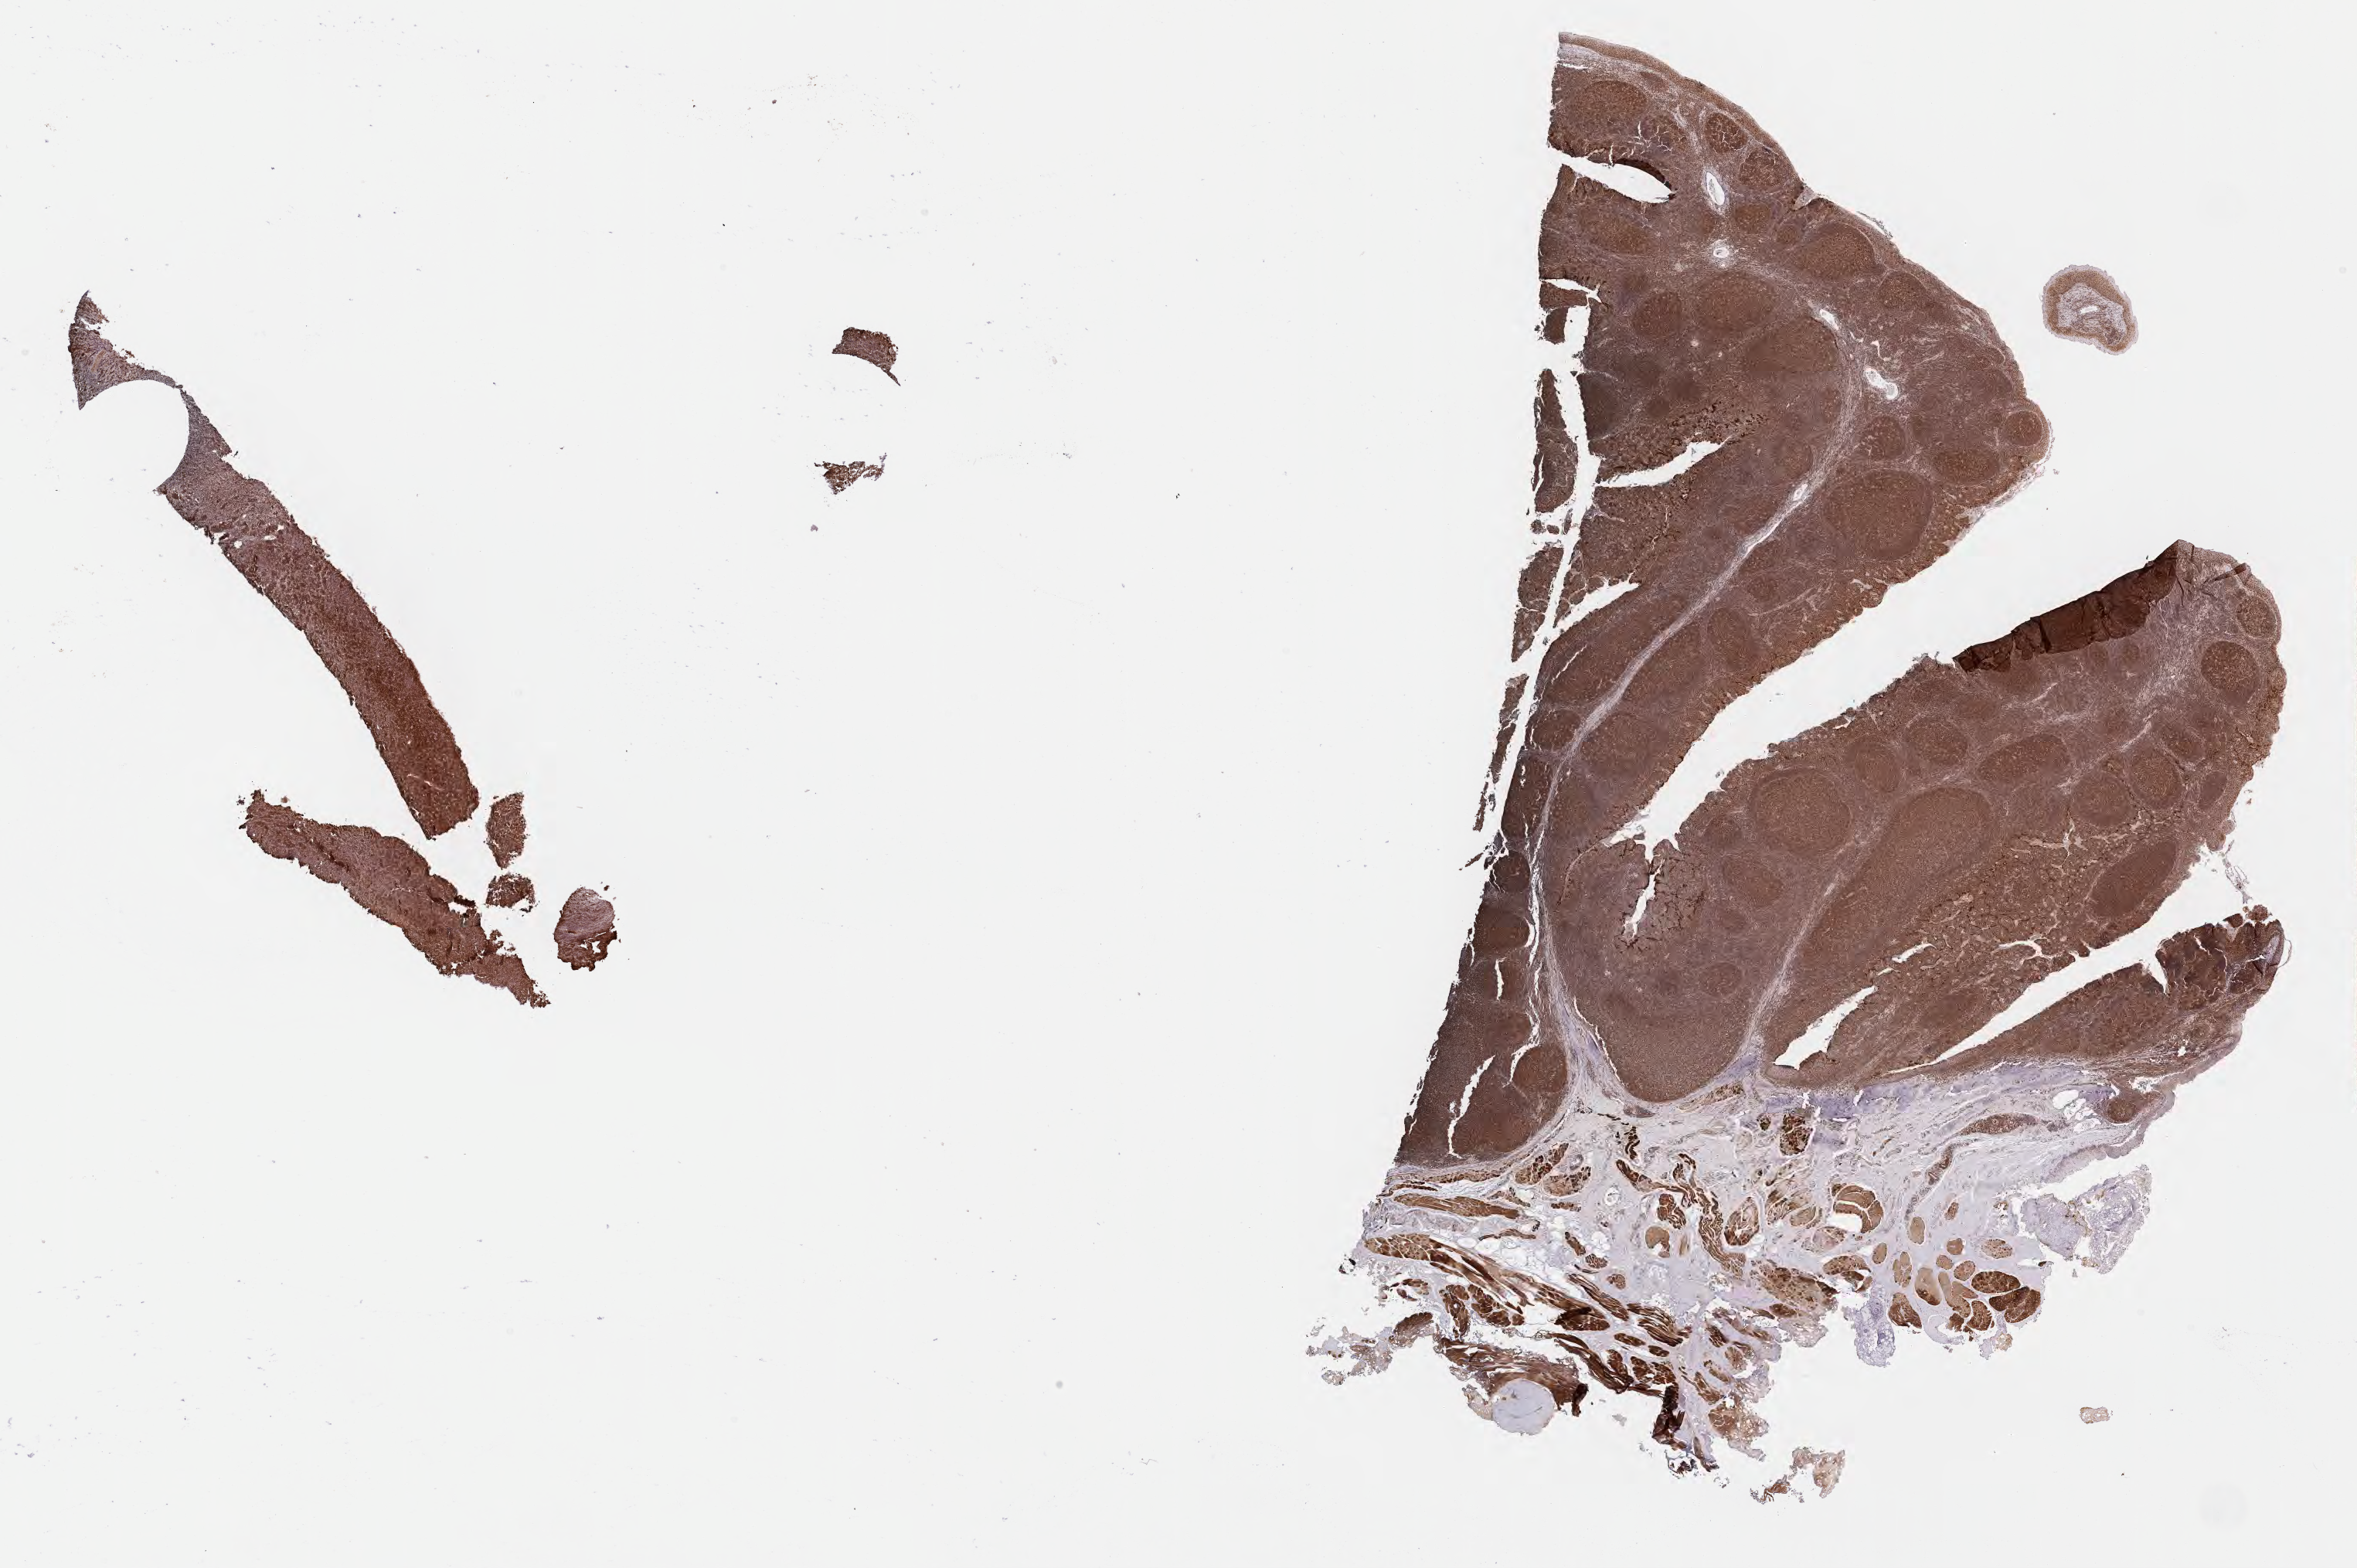
IHC for BCL6, whole-slide image — a low-resolution overview of the entire scanned area, about 24.7 x 16.4 mm. Specimen: tumor tissue. Site: liver. Male patient, age 15 years.
* histologic diagnosis: Burkitt lymphoma, NOS